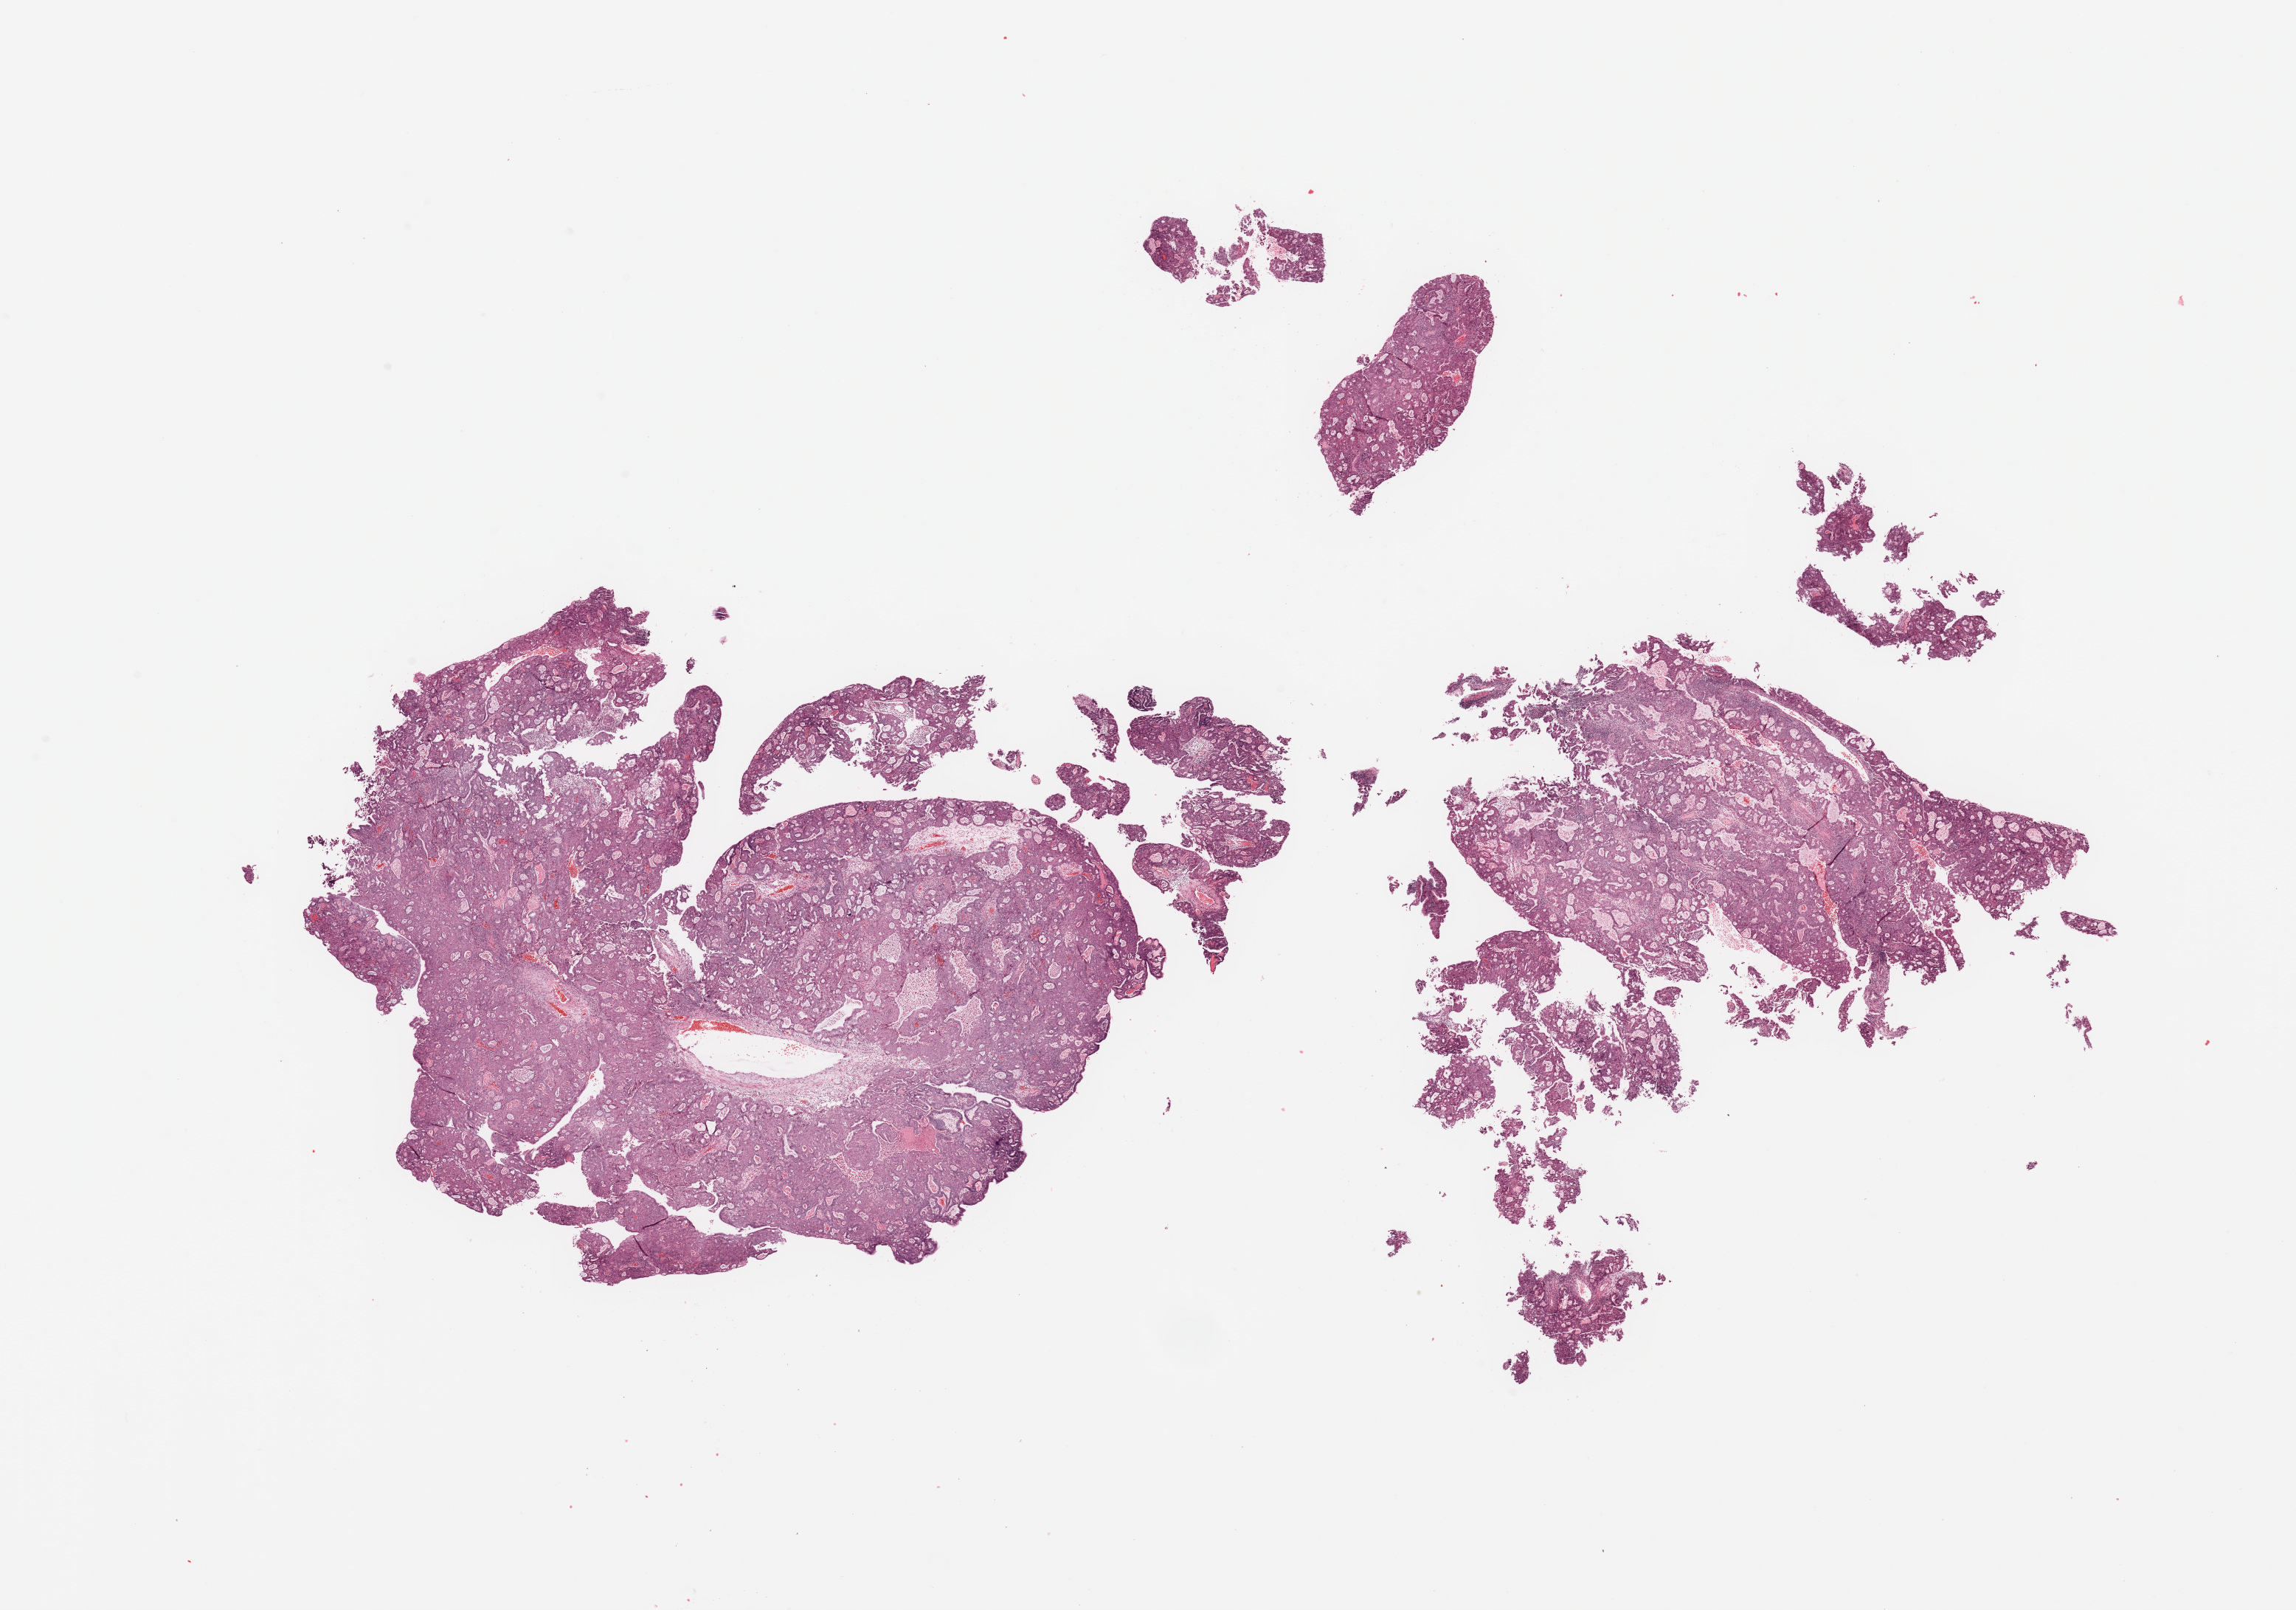
Digitized H&E tissue section (whole slide), a low-resolution overview of the entire scanned area, about 24.6 x 17.3 mm (slide scanned at 20x); tumour tissue sample, sampled site: uterus. Female, 60 y/o. Histologic grade: G1 (well differentiated). Composition of this section per pathologist review: tumour nuclei 85%, necrosis 0%.
- AJCC pathologic stage: I
- diagnosis: Endometrioid adenocarcinoma, NOS